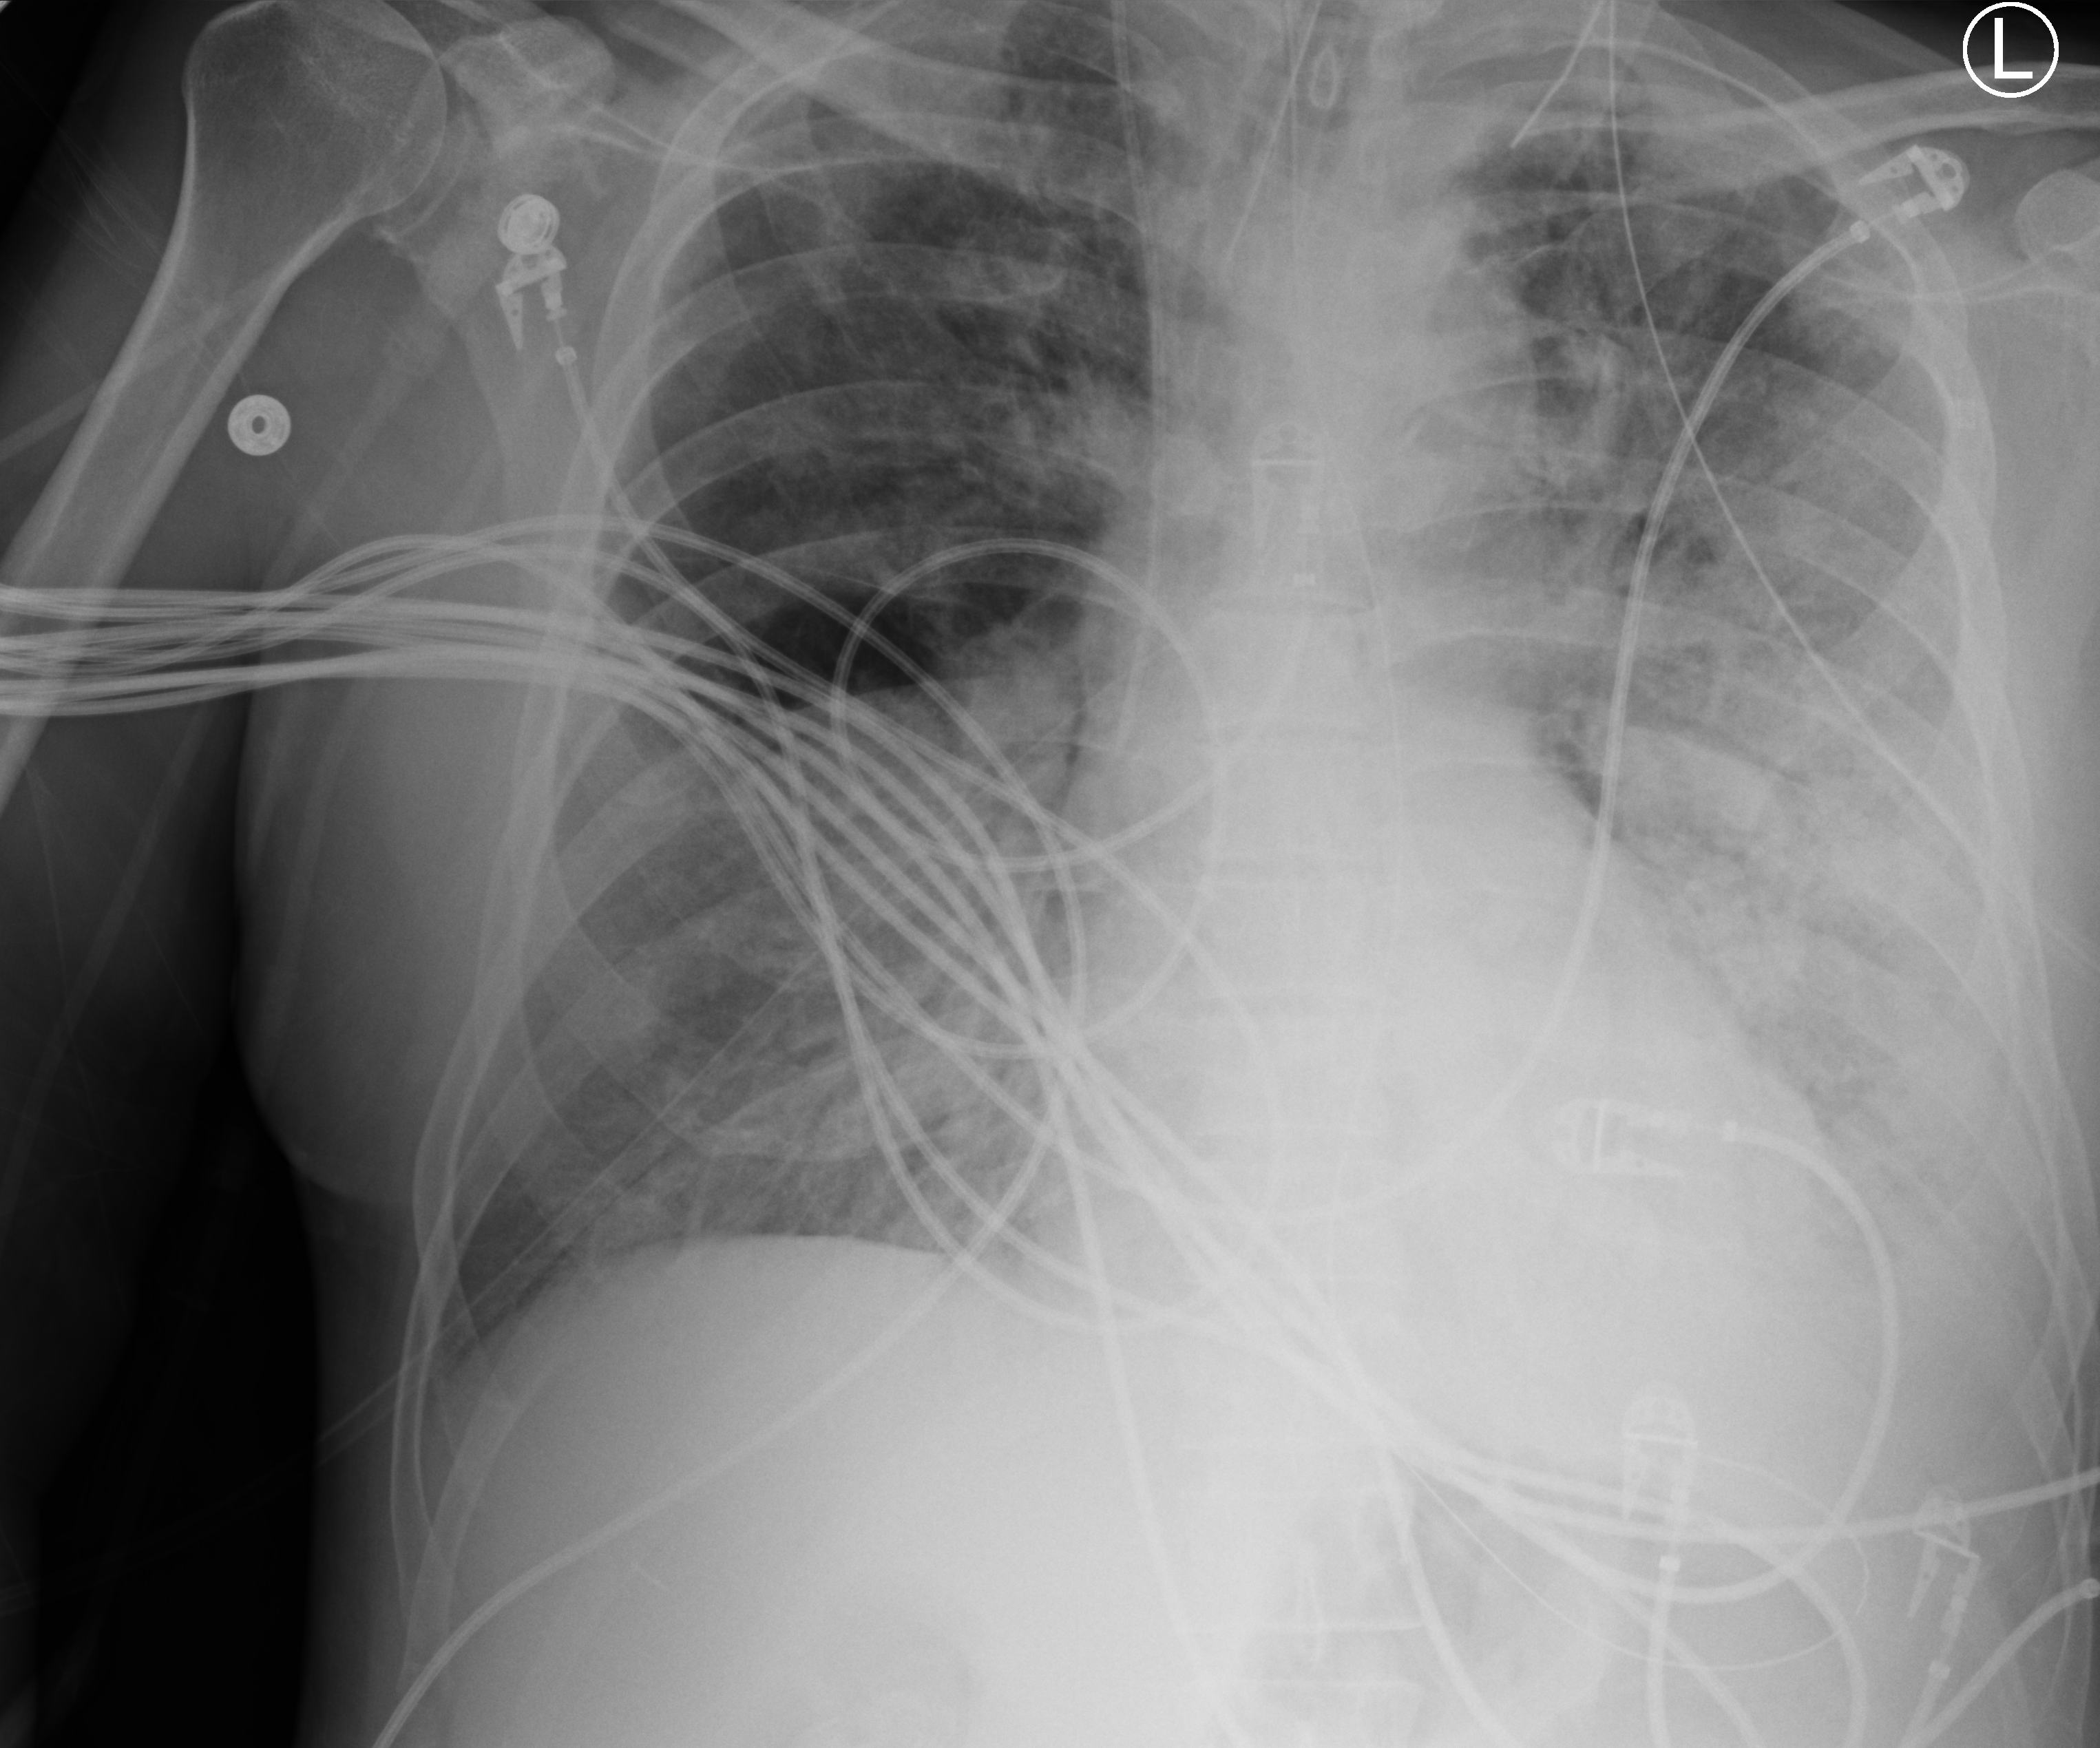
Portable chest radiograph; anteroposterior (AP) projection. Male patient hospitalised with COVID-19, age 60–74 years.
Hospital-stay facts (about this admission, not read from this image; timing relative to this image not recorded):
- mechanically ventilated during this hospital stay: yes
- admitted to intensive care during this hospital stay: yes